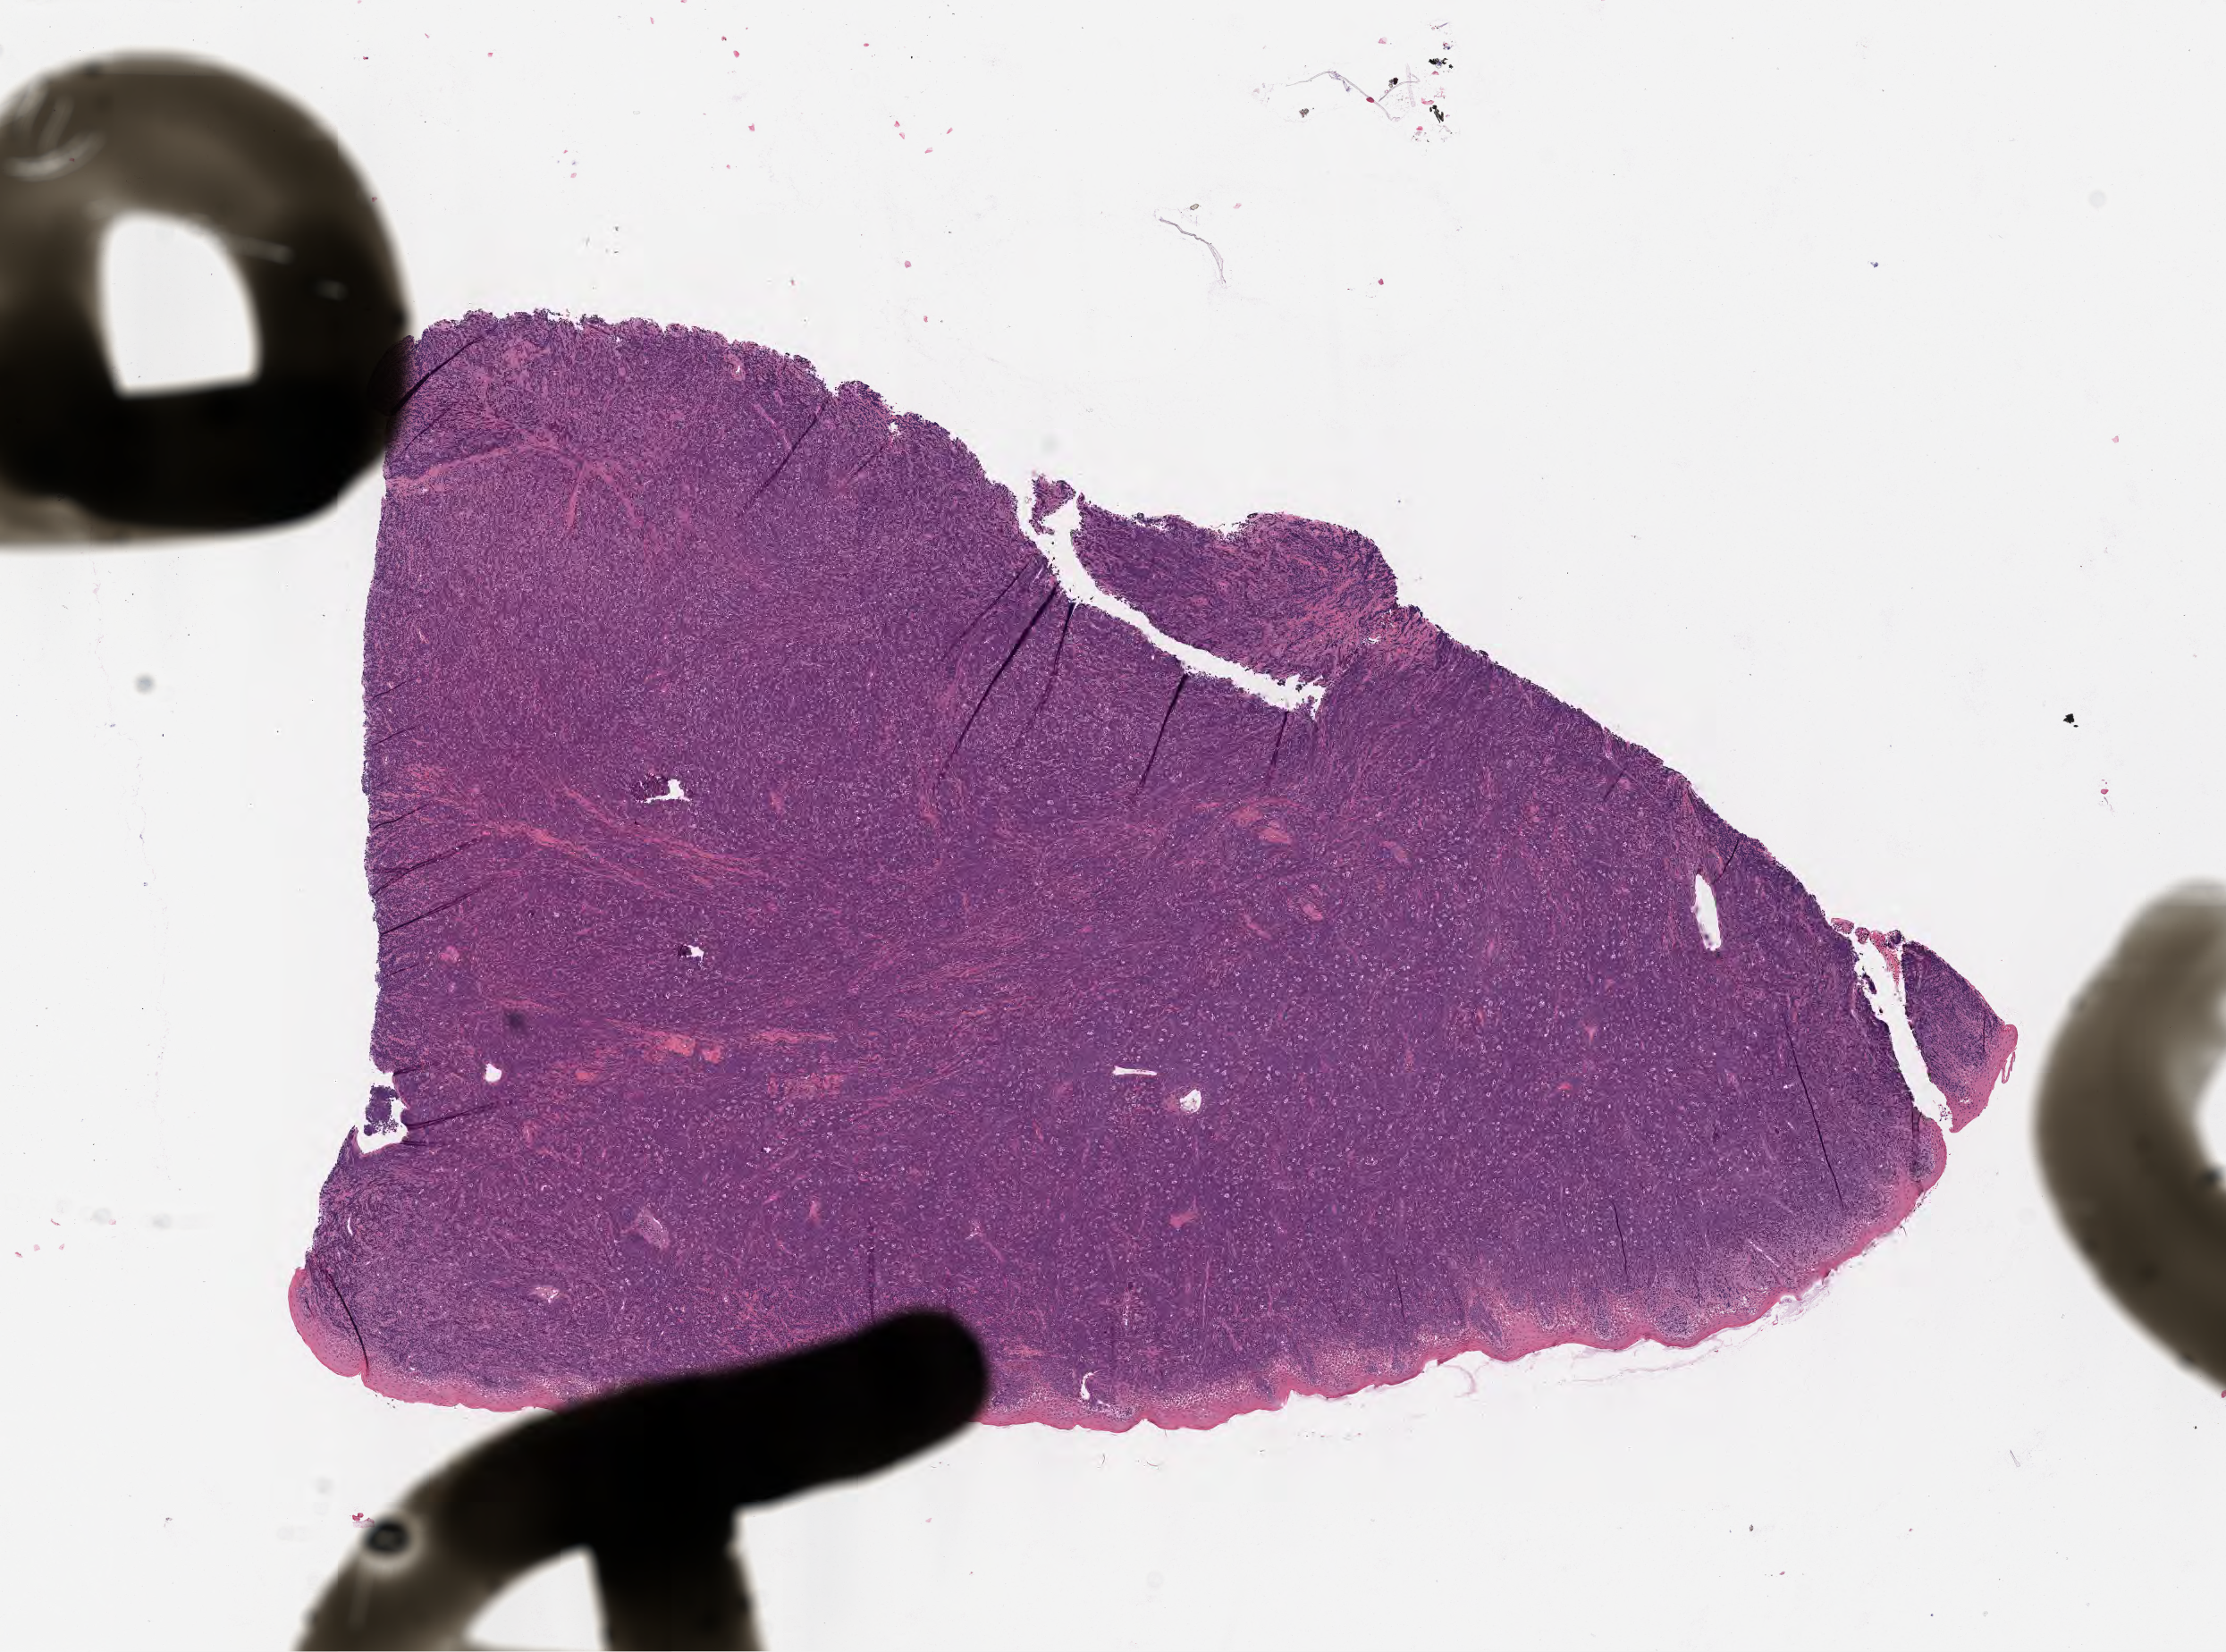
Digitized H&E-stained section, low-resolution overview of the scanned area, about 10.1 x 7.5 mm. Tumor tissue. Anatomic site: cranium. Male patient, aged 13.
• diagnosis: Diffuse large B-cell lymphoma, NOS